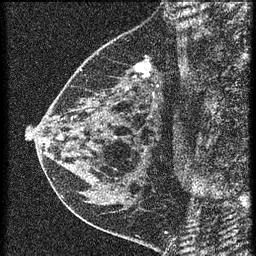
Breast MRI (dynamic contrast-enhanced), one sagittal slice; position 23 of 60 along the scan axis; 3 images stored at this slice position (order not interpretable as contrast timing); 1.5 T; TE 4.2 ms, TR 20.4 ms; 1.5 mm slice thickness; 256 × 256 image matrix, field of view 180 × 180 mm. Patient: female, 46 years. Case-level facts recorded for this patient, not image findings: setting: breast cancer imaged before/during neoadjuvant chemotherapy; receptor status: HR-positive, HER2-negative.
Annotated regions visible in this slice (semi-automatic segmentation, software-assisted and operator-edited):
- analysis volume of interest (the breast-tissue region the enhancement analysis was run in; not a lesion): box from (x=58, y=36) to (x=169, y=155) px
- tumour enhancement mask (voxels above the 90 % enhancement threshold inside the analysis volume of interest): (x=138, y=64)–(x=151, y=75)